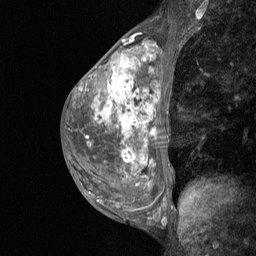
Breast MRI (dynamic contrast-enhanced), one sagittal slice; position 29 of 64 along the scan axis; dynamic contrast-enhanced study with each time point stored as its own series, time point 2 of 3 at this slice position (early post-contrast, ordered by acquisition time); 1.5 T; TE 4.8 ms, TR 27 ms; 256 × 256 image matrix, field of view 200 × 200 mm. Female patient, age 36 years. From the clinical record (not read from this slice): setting: breast cancer imaged before/during neoadjuvant chemotherapy; receptor status: HR-positive, HER2-negative.
Outlined on this slice (semi-automatic segmentation, software-assisted and operator-edited):
- analysis volume of interest (the breast-tissue region the enhancement analysis was run in; not a lesion): bounding box <73,45,170,210> (left, top, right, bottom; pixels)
- tumour enhancement mask (voxels above the 90 % enhancement threshold inside the analysis volume of interest): <115,77,117,79>